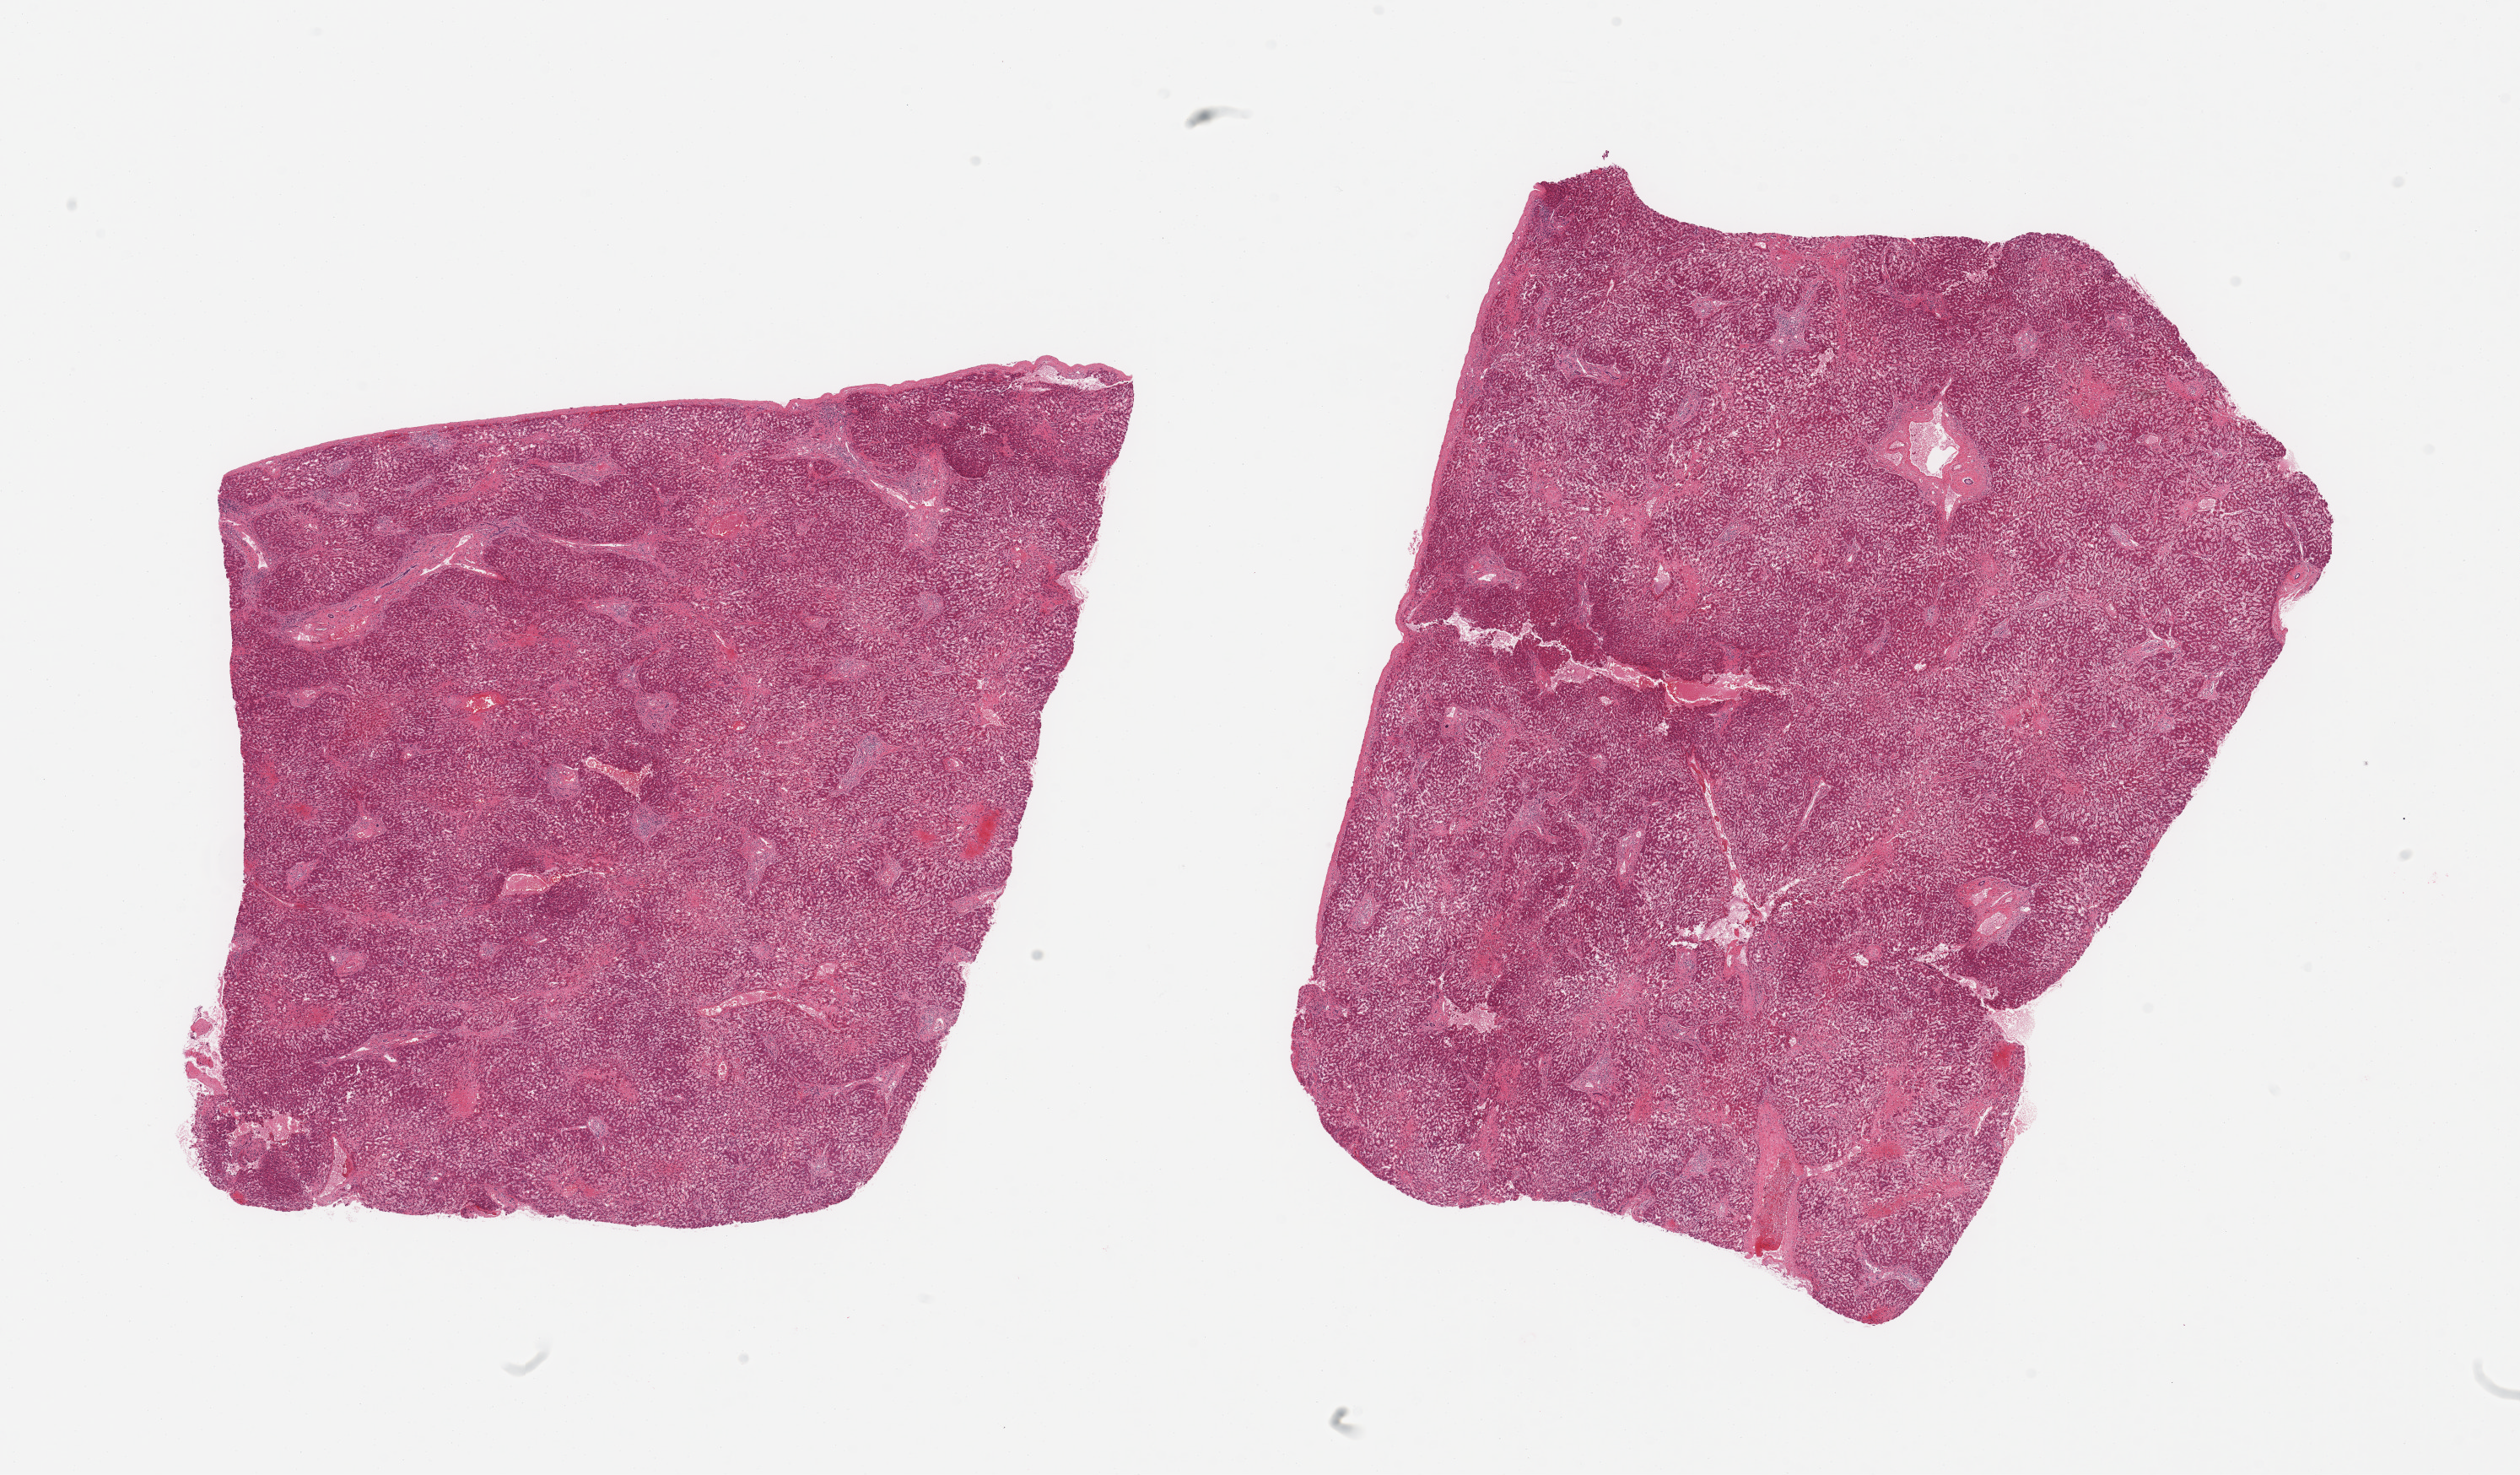
H&E whole-slide image, brightfield — a low-resolution overview of the entire scanned area, about 23.6 x 13.8 mm; PAXgene-fixed paraffin-embedded (PFPE) section; section of liver (target tissue); tissue donor sample. Donor sex: male.
• pathologist's review note for this sample: 2 pieces, moderate fibrosis, cardiac congestion and chronic hepatitis